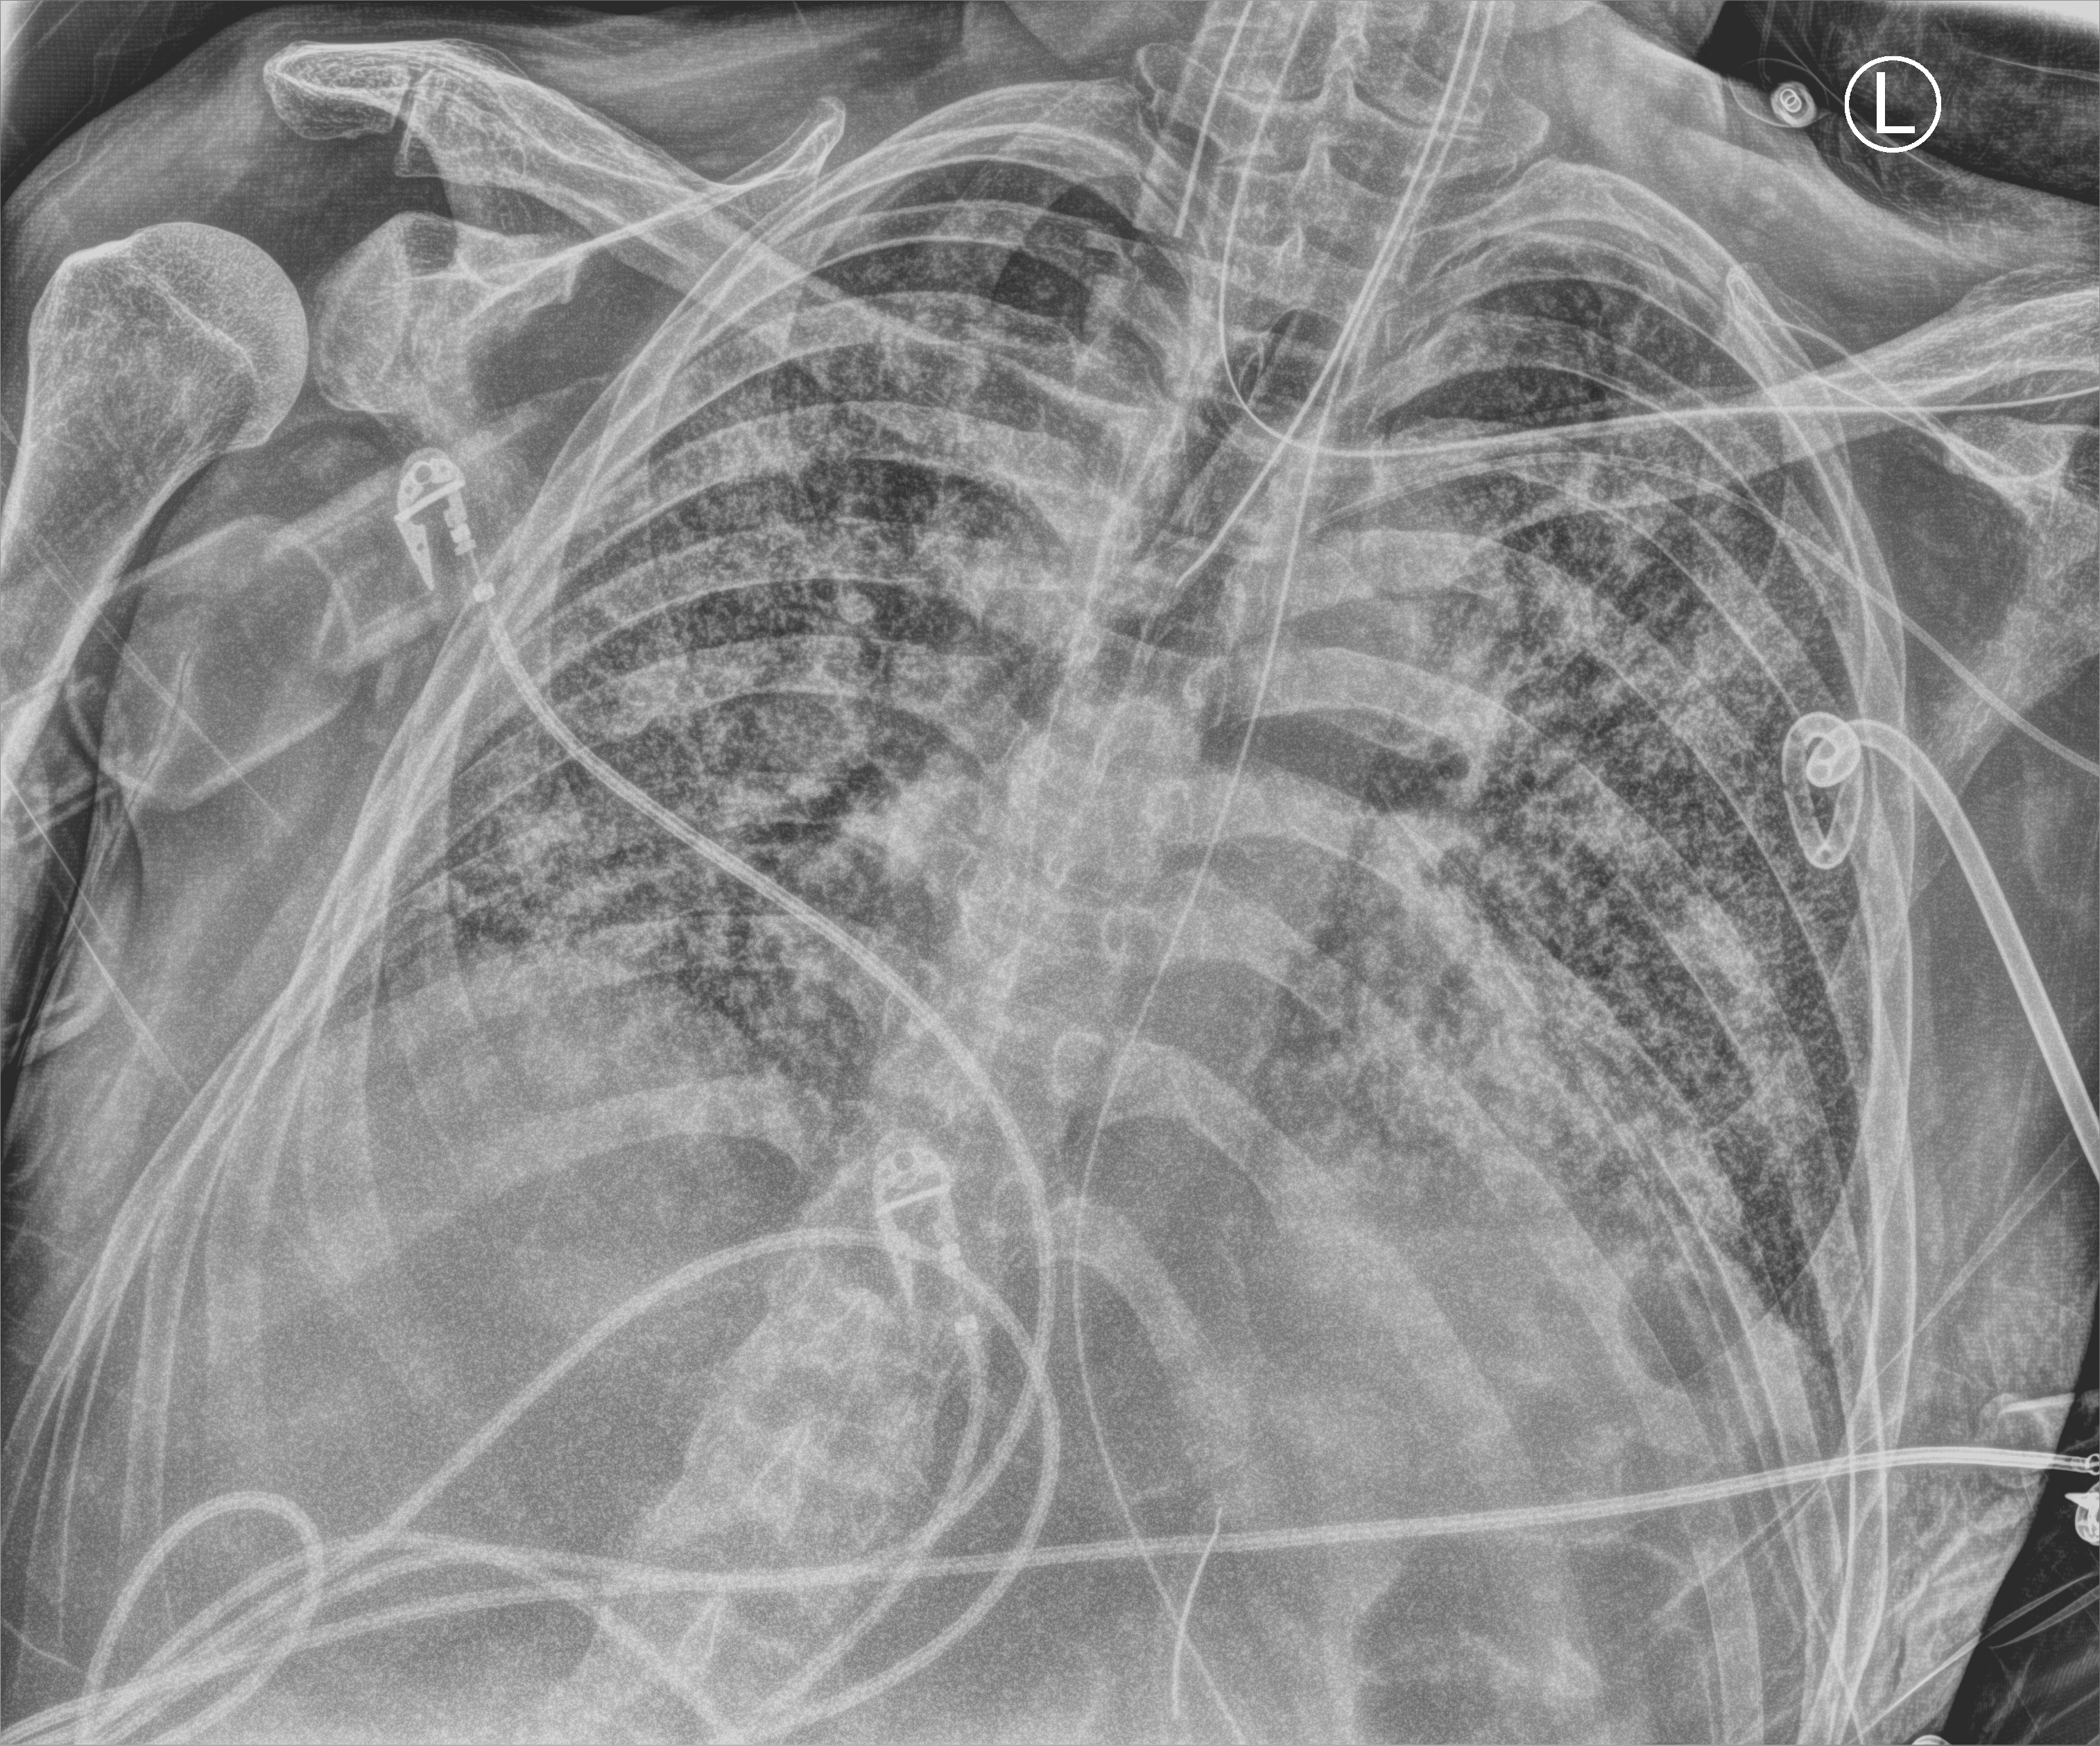
Portable chest radiograph; anteroposterior (AP) projection. Patient hospitalised with COVID-19; male, aged 60–74 years.
Admission-level facts for this patient (not findings on this image; timing relative to this image not recorded): mechanically ventilated during this hospital stay: yes.